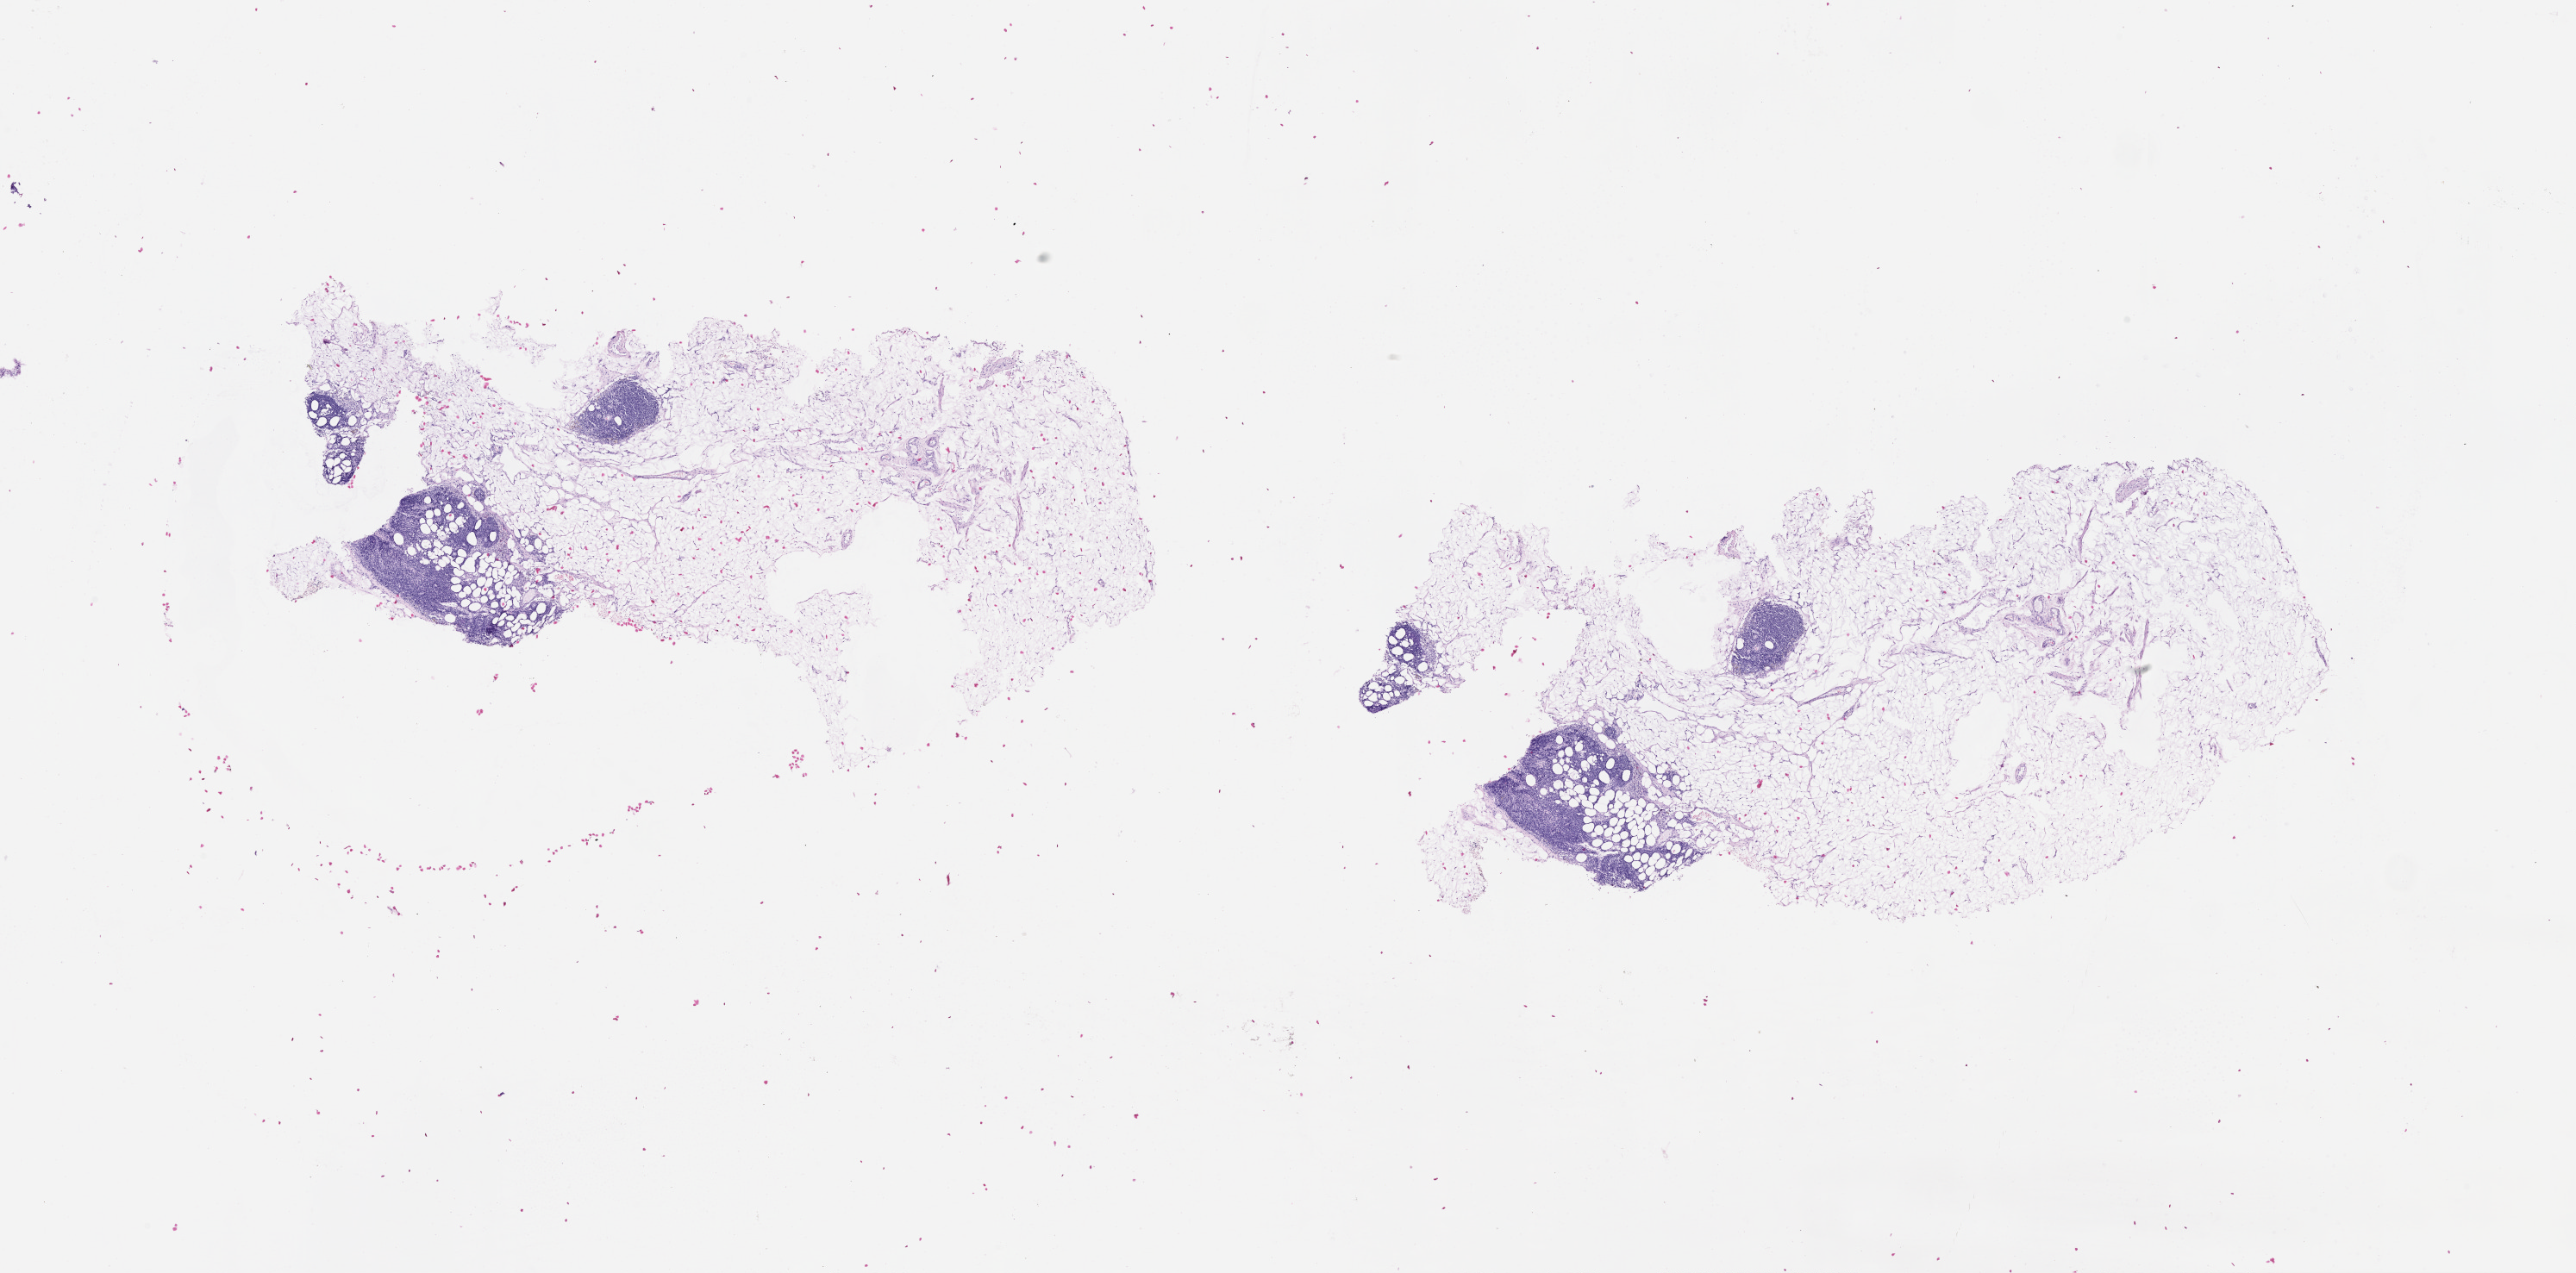
Hematoxylin and eosin (H&E) stained whole-slide image, shown as a low-resolution overview of the whole scanned area (about 24.1 x 11.9 mm, slide scanned at 20x). 72-year-old male patient.
Patient diagnosis: Malignant melanoma, NOS.